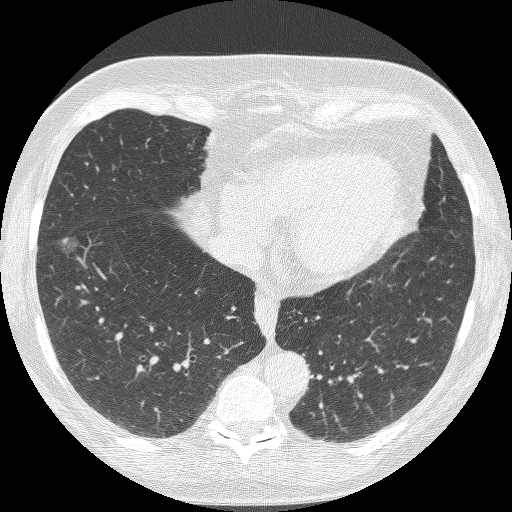
Low-dose screening chest CT, axial slice, baseline screening round, lung window (W 1500 / L -600 HU), 1.25 mm slice thickness, slice 74 of 221 in the series, 512 × 512 image matrix. Female, age 68 years at enrolment. Current smoker at enrolment.
Expert-annotated lung lesion, bounding box (x1, y1, x2, y2) in pixels: (32, 227, 84, 281). Screening reader's record for this exam (one nodule recorded; not confirmed to be the boxed lesion): non-calcified nodule or mass ≥4 mm, right lower lobe, 16 × 12 mm, poorly defined margins, ground glass attenuation. Participant outcome: lung cancer diagnosed 406 days after this screen — bronchiolo-alveolar adenocarcinoma, NOS, right lower lobe, well differentiated (G1), stage IA (AJCC 6th edition), 13 mm at pathology.